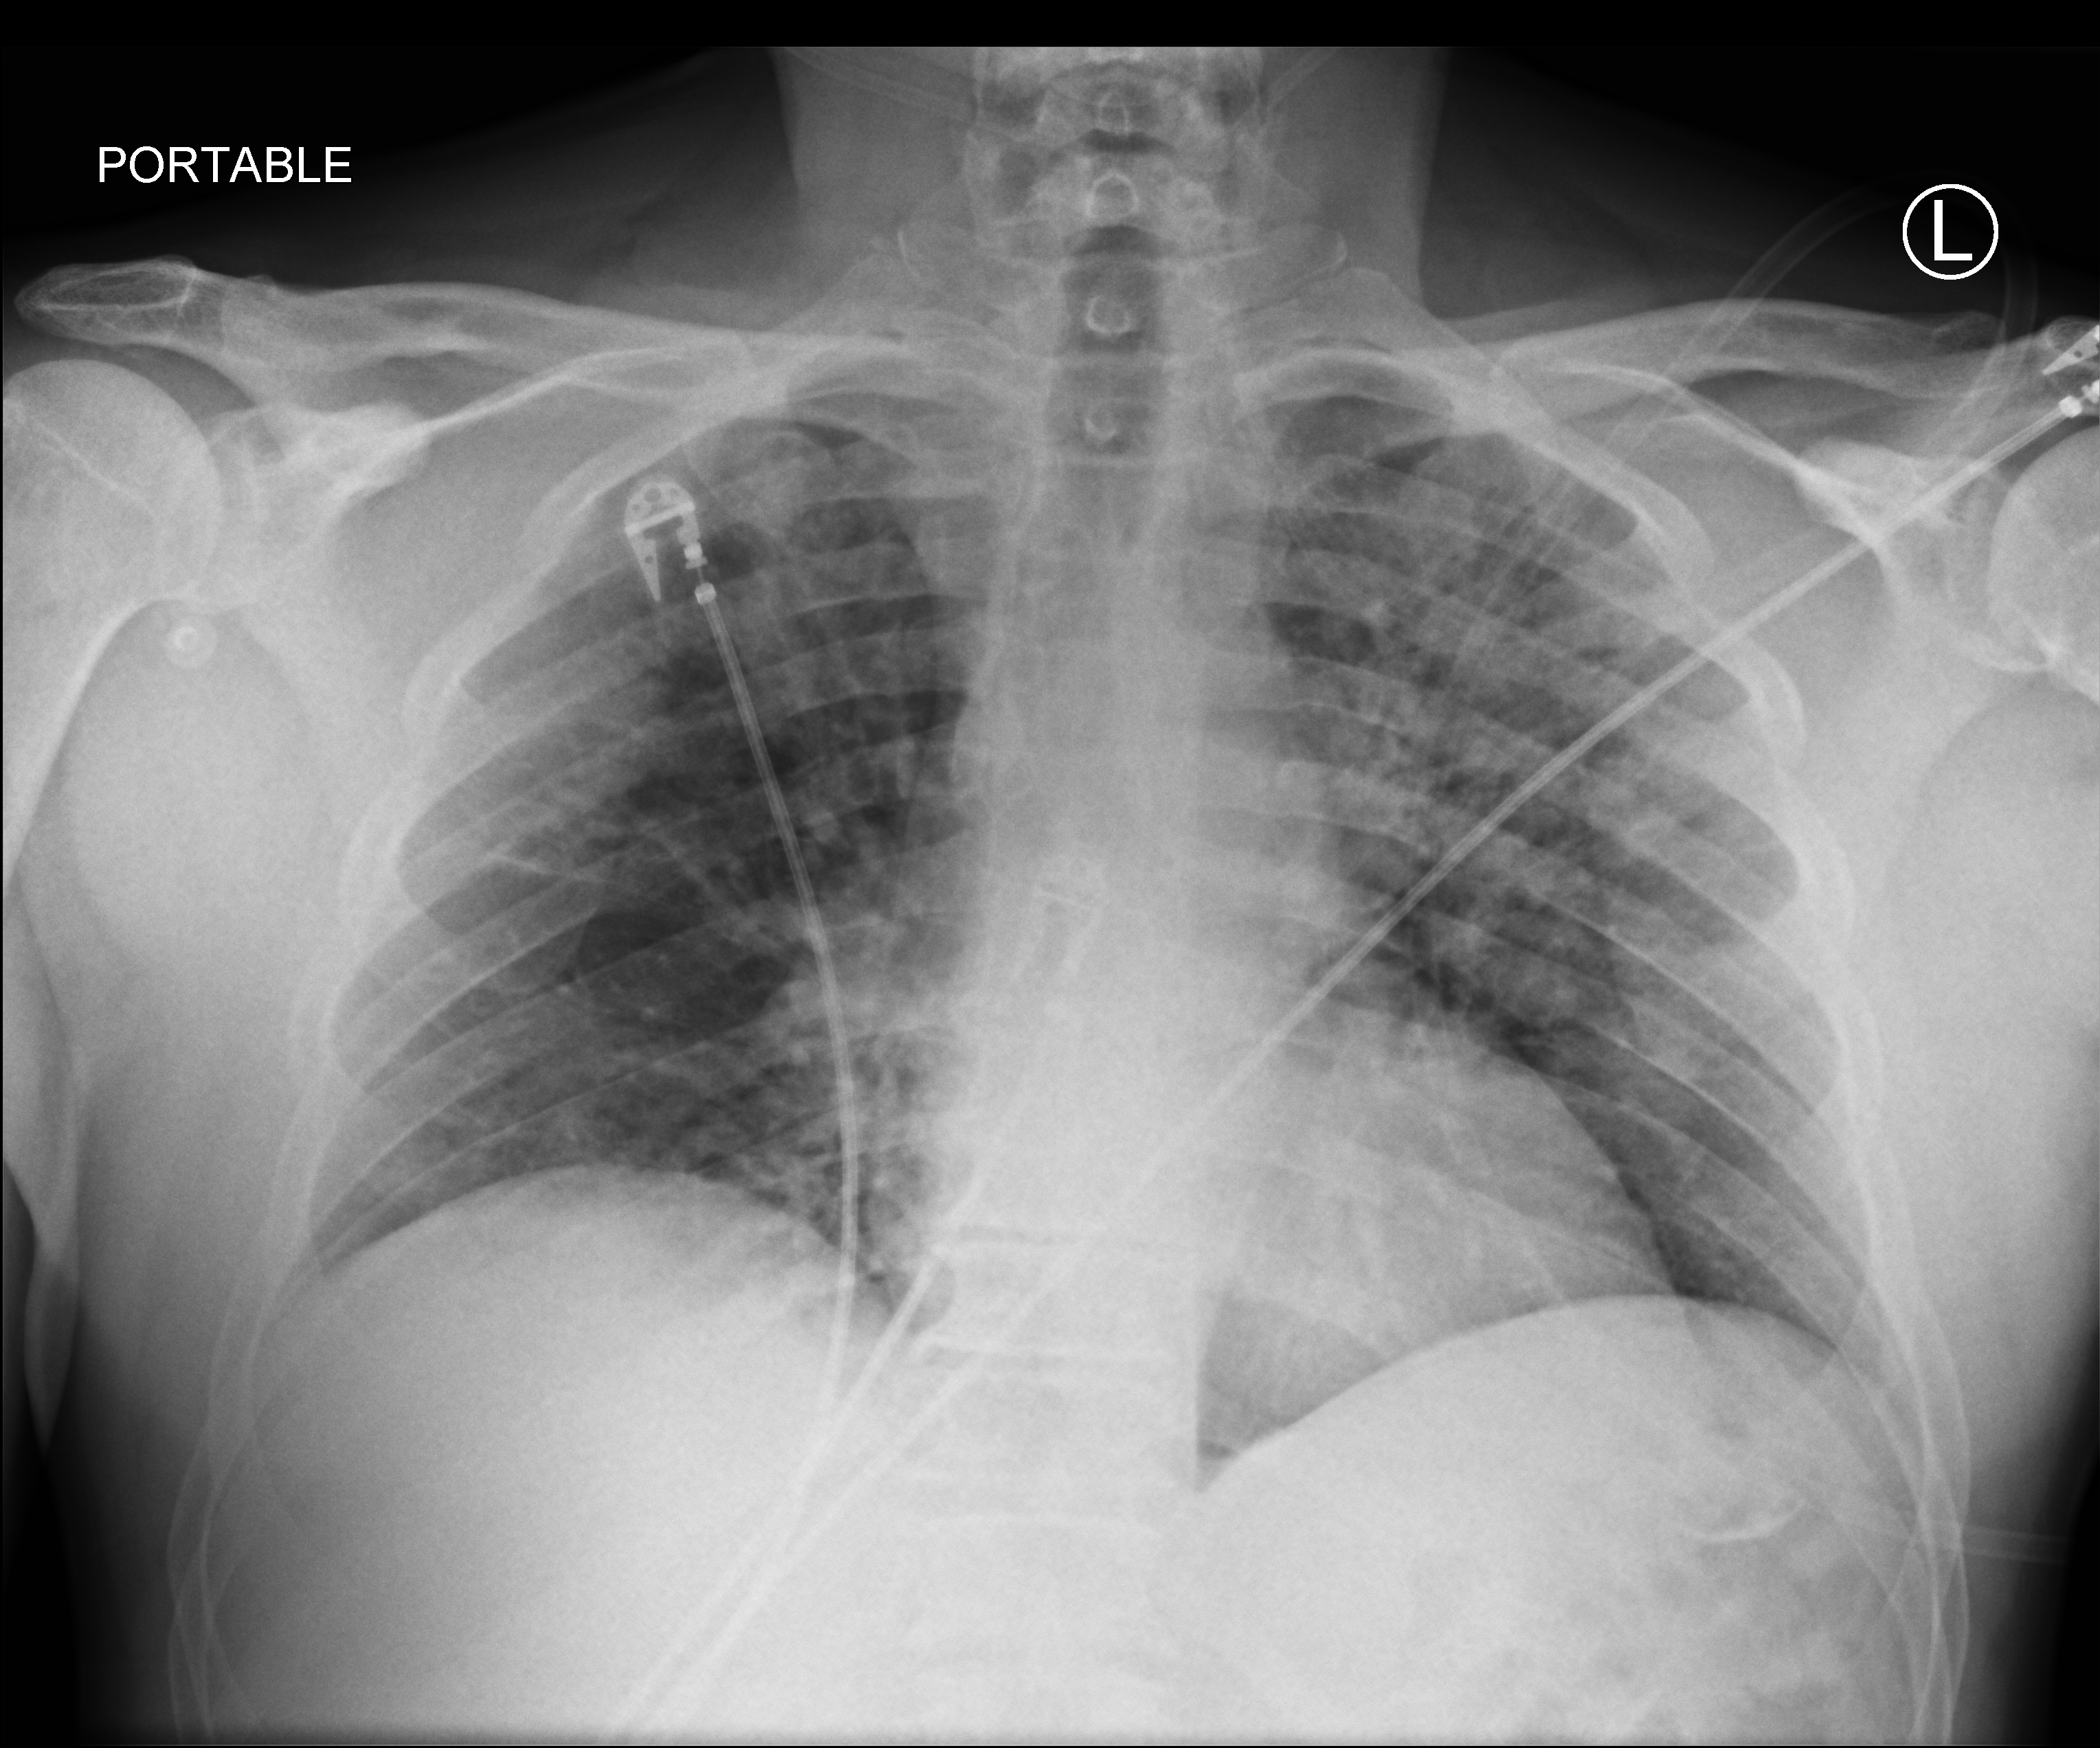
Chest X-ray (portable); anteroposterior (AP) projection. Patient hospitalised with COVID-19; male, aged 18–59 years.
From the hospital-stay record, not from the radiograph (when in the stay this image was taken is not recorded): mechanically ventilated during this hospital stay: no; smoking status (admission record): never.